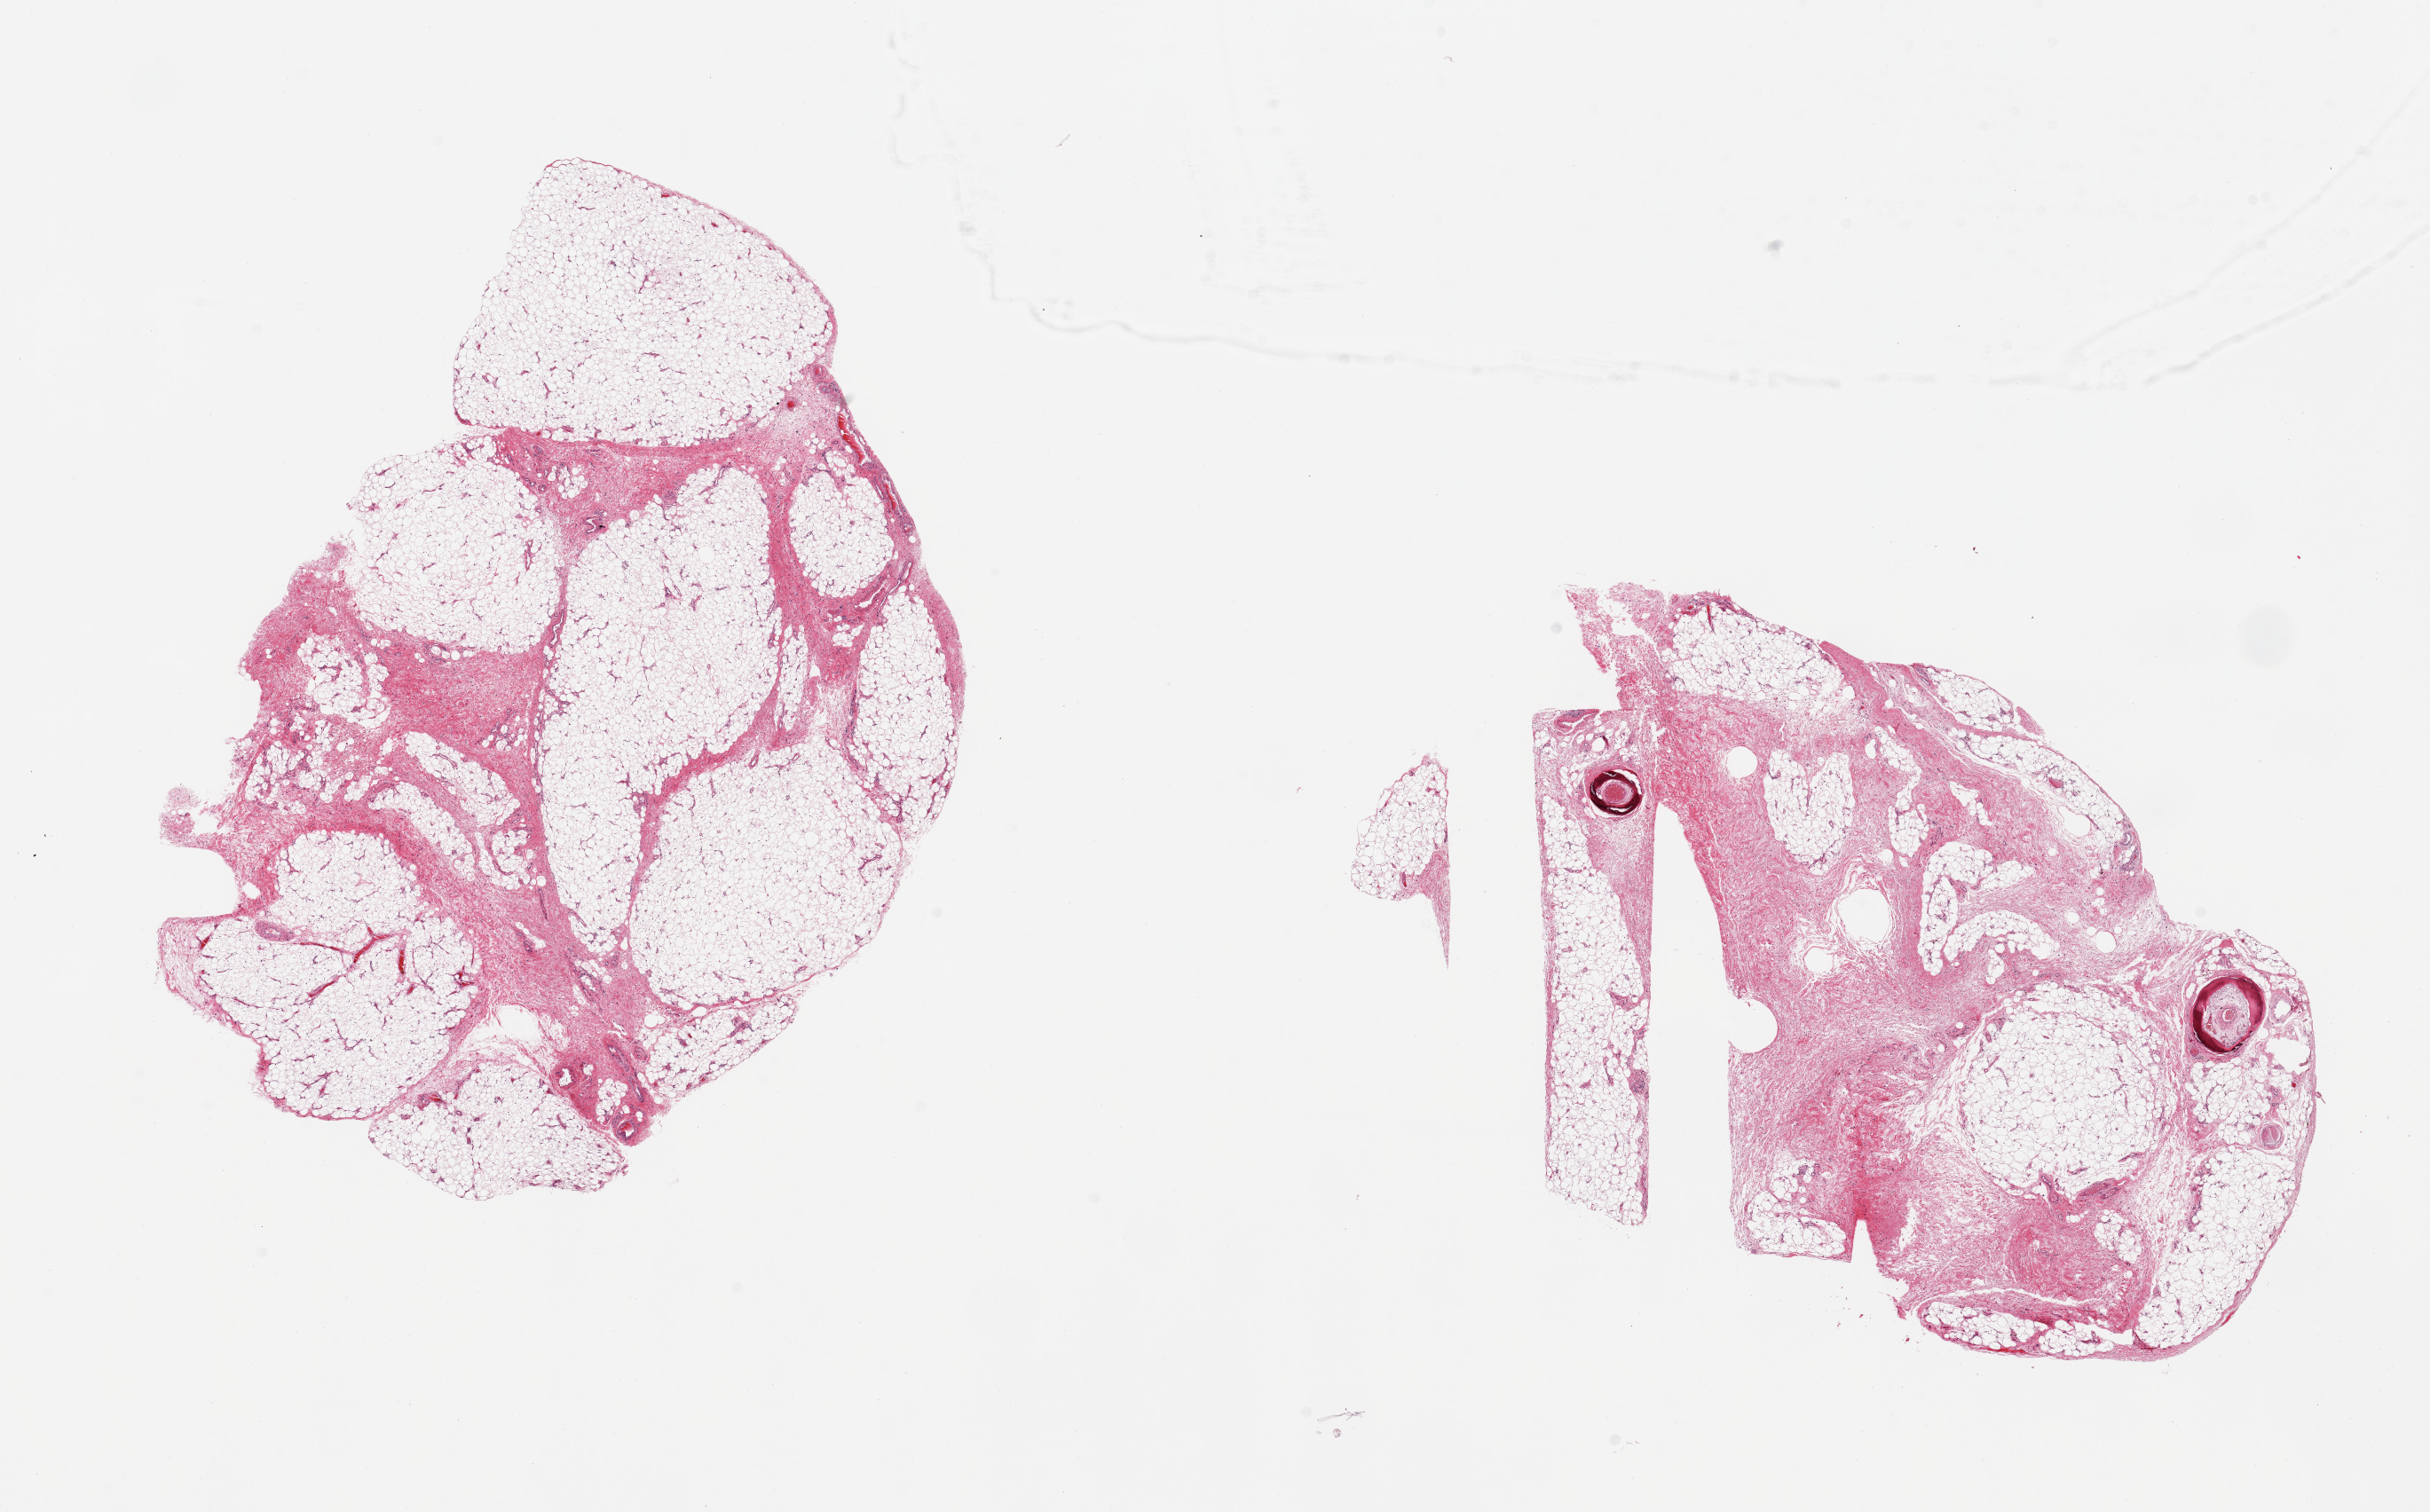
Haematoxylin and eosin whole-slide image — a low-resolution overview of the entire scanned area, about 21.7 x 13.5 mm (acquisition: 20x scan). PAXgene-fixed, paraffin-embedded tissue. Section of adipose tissue (target tissue). Tissue donor sample. Donor: male.
• review note (as recorded): 2 pieces, ~40-50% fascia, evidence of old fat necrosis